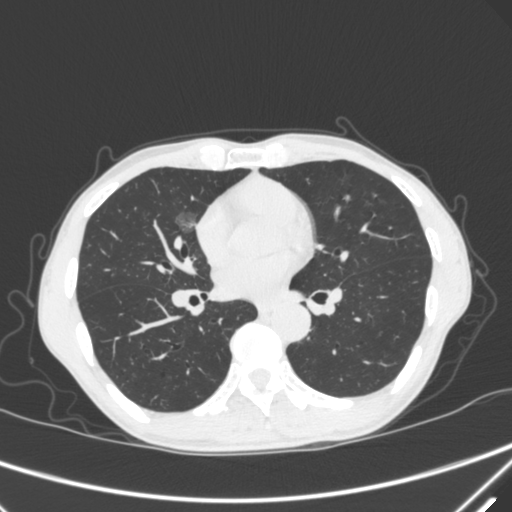
Chest CT, one axial slice. 120 kVp. Lung window (W 1500 / L -600 HU). 1 mm slice thickness. 512 × 512 image matrix, field of view 350 × 350 mm. Male patient, age 67 years. Case-level facts recorded for this patient, not image findings: clinical TNM (as recorded): T1c N0 M0; histopathological grade: G1-2.
Annotated regions visible in this slice (bounding box drawn by a radiologist):
- lung tumour (recorded histology: adenocarcinoma): bounding box (x1, y1, x2, y2) in pixels: (168, 205, 204, 242)